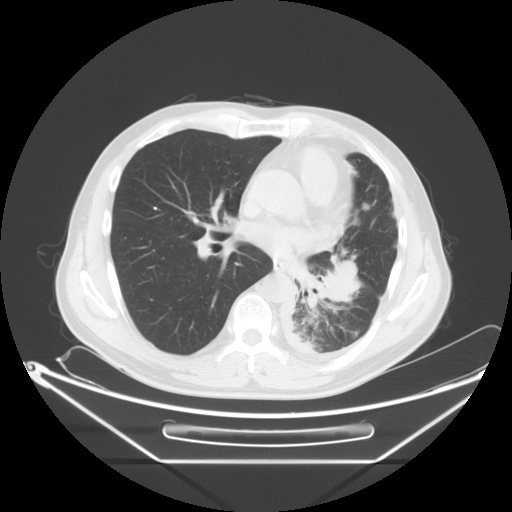
Chest CT, one axial slice; position 31 of 63 along the scan axis; lung window (W 1500 / L -600 HU); 5 mm slice thickness; 512 × 512 image matrix, field of view 442 × 442 mm. Male patient, age 60 years. Case-level facts recorded for this patient, not image findings: clinical TNM (as recorded): T4 N1 M1.
Annotated regions visible in this slice (rectangle marked by the reading radiologist):
- lung tumour (recorded histology: adenocarcinoma): bounding box [x1, y1, x2, y2] px = [303, 259, 366, 318]